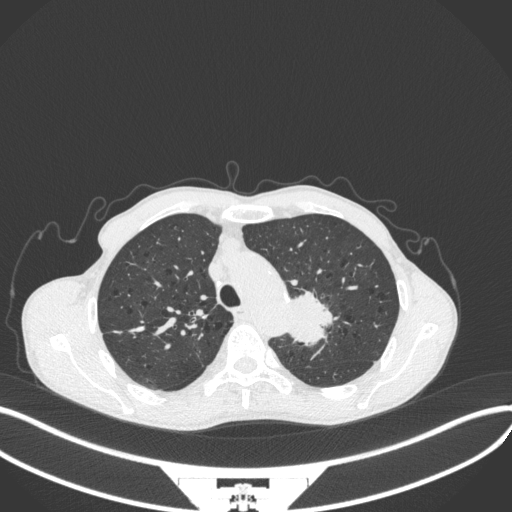
Chest CT, one axial slice; slice 317 of 394 in the series (ordered by position); 120 kVp; lung window (W 1500 / L -600 HU); 512 × 512 image matrix. Male patient, age 65 years. Case-level facts recorded for this patient, not image findings: clinical TNM (as recorded): T2b N0 M0; histopathological grade: G2.
Structures marked on this image (bounding box drawn by a radiologist):
- lung tumour (recorded histology: adenocarcinoma): bounding box [x1, y1, x2, y2] px = [285, 278, 333, 353]